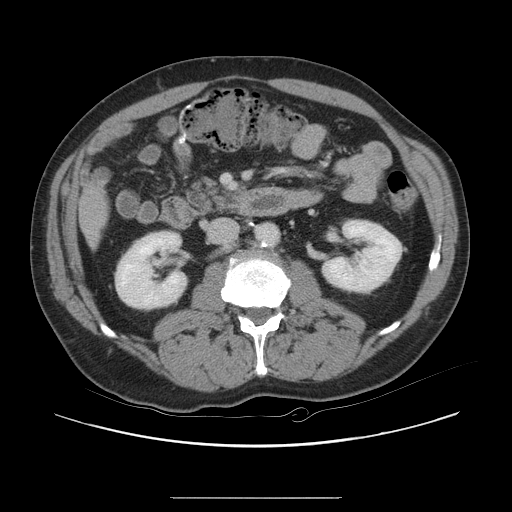
Contrast-enhanced abdominal CT, one axial slice; position 3 of 40 along the scan axis; soft-tissue window (W 400 / L 40 HU); 5 mm slice thickness; 512 × 512 image matrix, field of view 408 × 408 mm. Male patient, age 64 years. Case-level facts recorded for this patient, not image findings: diagnosis: colorectal cancer liver metastases, imaged before liver resection.
Outlined on this slice (manually delineated by an expert):
- liver: box from (x=83, y=192) to (x=104, y=240) px